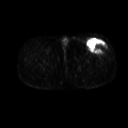
FDG PET of an extremity soft-tissue mass (from a PET/CT study), one axial slice; slice 245 of 267 in the series (ordered by position); 3.27 mm slice thickness; 128 × 128 image matrix. Patient: male, 64 years. Case-level facts recorded for this patient, not image findings: histological type: extraskeletal osteosarcoma; grade: high; site of the primary tumour: thigh.
Structures marked on this image (expert contour drawn on MRI and transferred to this co-registered scan by the dataset authors):
- gross tumour volume (mass): bounding box (x1, y1, x2, y2) in pixels: (88, 40, 107, 53)